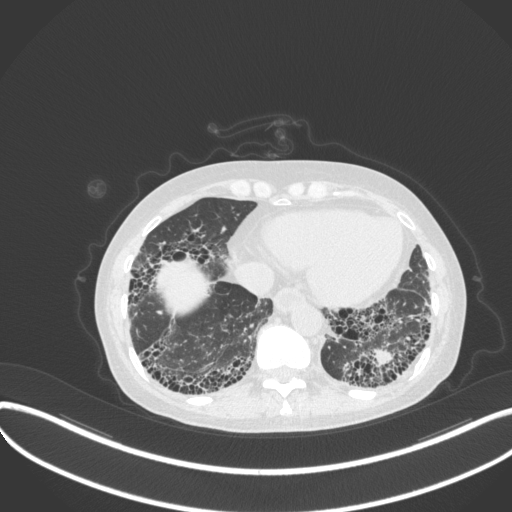
Chest CT, one axial slice; position 74 of 373 along the scan axis; reconstruction kernel B31f; 120 kVp; lung window (W 1500 / L -600 HU); 512 × 512 image matrix, field of view 400 × 400 mm. Female patient, age 56 years. Case-level facts recorded for this patient, not image findings: clinical TNM (as recorded): T1 N0 M0.
Annotated regions visible in this slice (rectangle marked by the reading radiologist):
- lung tumour (recorded histology: adenocarcinoma): box from (x=370, y=348) to (x=397, y=370) px